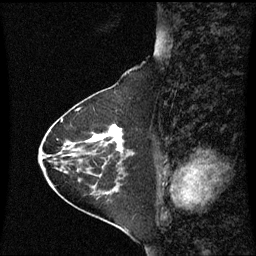
Breast MRI (dynamic contrast-enhanced), one sagittal slice; dynamic contrast-enhanced series, image 2 of 3 at this slice position (ordered by acquisition); 1.5 T; TE 4.2 ms, TR 8.9 ms; 256 × 256 image matrix, field of view 210 × 210 mm. Female patient, age 63 years. From the clinical record (not read from this slice): setting: breast cancer imaged before/during neoadjuvant chemotherapy; receptor status: HR-positive, HER2-negative.
Outlined on this slice (semi-automatic segmentation, software-assisted and operator-edited):
- analysis volume of interest (the breast-tissue region the enhancement analysis was run in; not a lesion): bounding box <88,126,128,163> (left, top, right, bottom; pixels)
- tumour enhancement mask (voxels above the 70 % enhancement threshold inside the analysis volume of interest): <92,126,124,152>